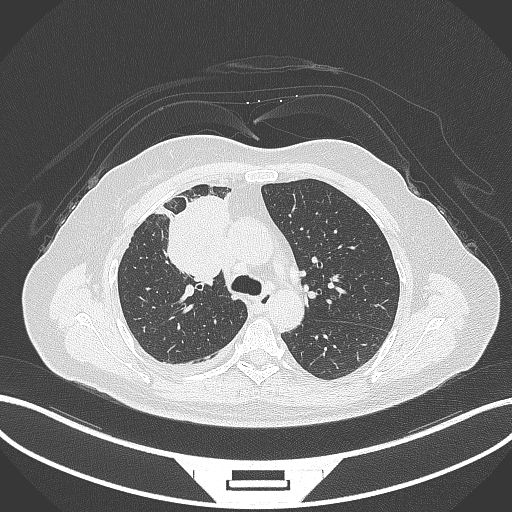
Chest CT, one axial slice; slice 192 of 305 in the series (ordered by position); reconstruction kernel B70f; 120 kVp; lung window (W 1500 / L -600 HU); 1 mm slice thickness; 512 × 512 image matrix. Female patient, age 52 years. Case-level facts recorded for this patient, not image findings: clinical TNM (as recorded): T3 N1 M1.
Outlined on this slice (rectangle marked by the reading radiologist):
- lung tumour (recorded histology: adenocarcinoma): bounding box (x1, y1, x2, y2) in pixels: (165, 185, 230, 286)